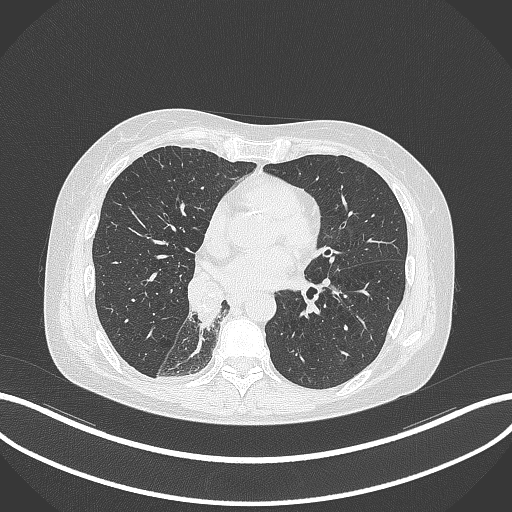
Chest CT, one axial slice. Position 139 of 329 along the scan axis. 120 kVp. Lung window (W 1500 / L -600 HU). 1 mm slice thickness. 512 × 512 image matrix, field of view 400 × 400 mm. Female patient, age 63 years. Case-level facts recorded for this patient, not image findings: clinical TNM (as recorded): T1c N0 M0.
Structures marked on this image (rectangle marked by the reading radiologist):
- lung tumour (recorded histology: adenocarcinoma): bounding box <187,273,222,328> (left, top, right, bottom; pixels)